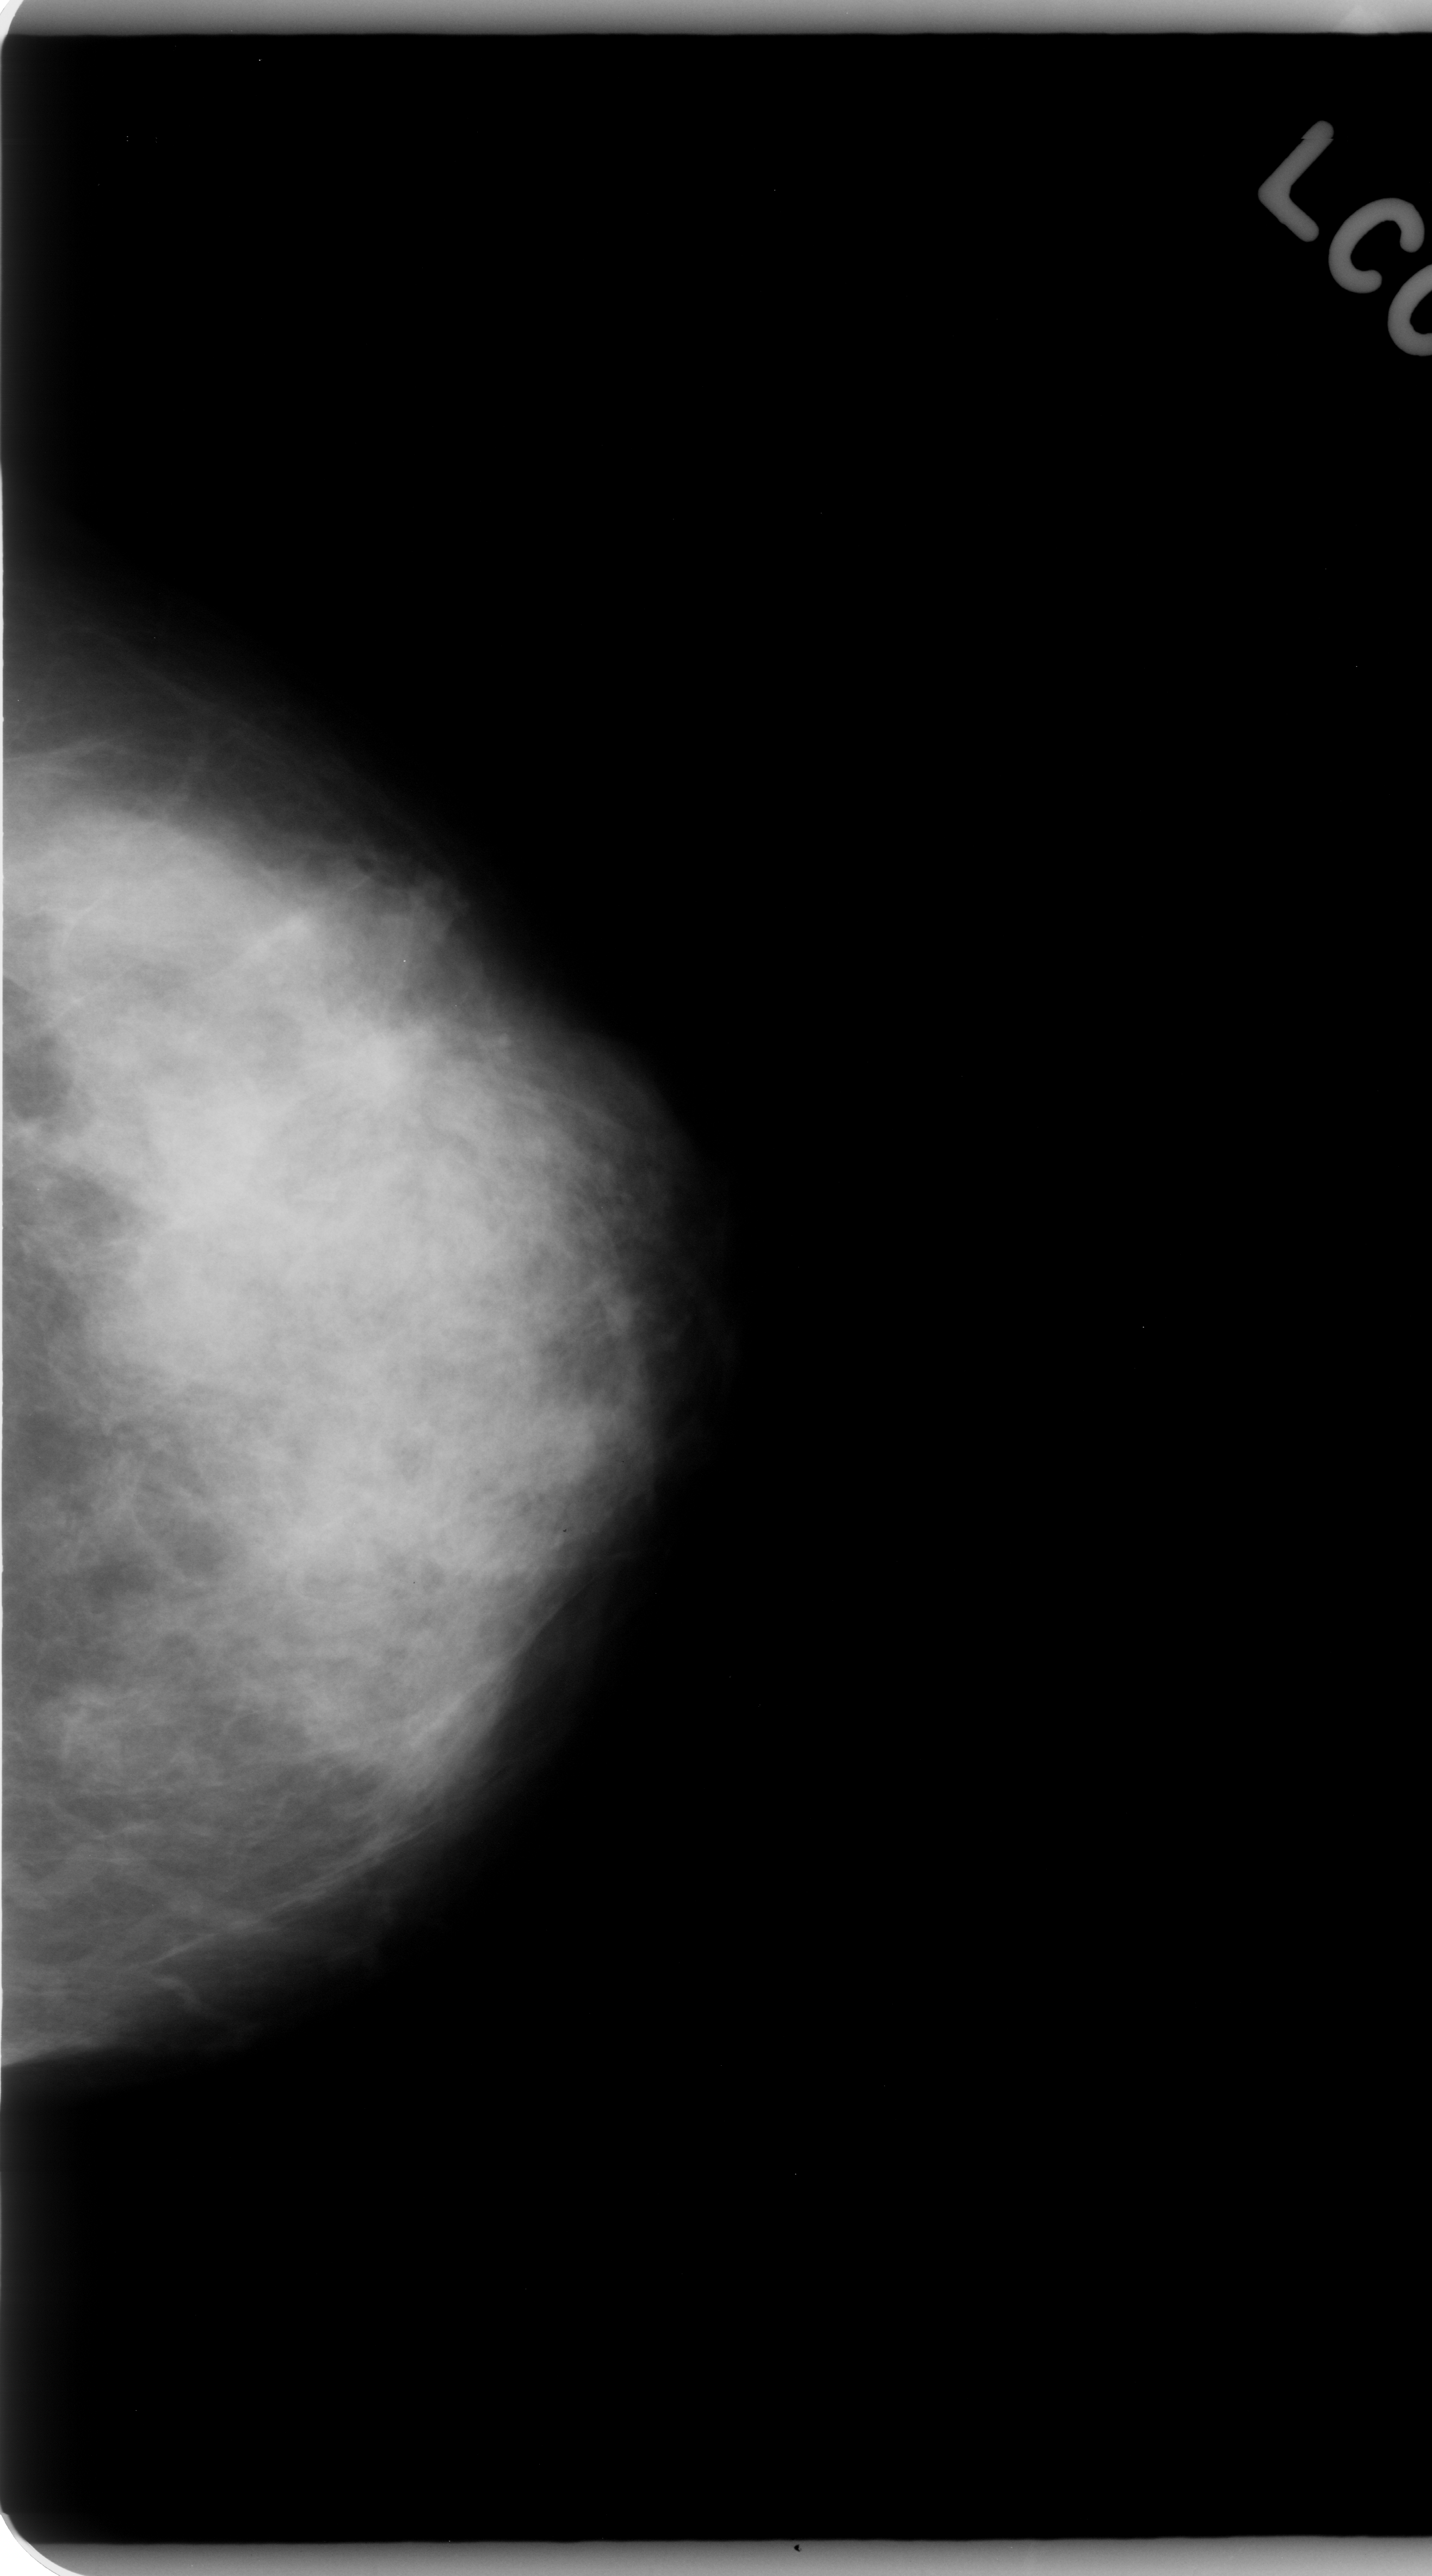
Scanned film-screen mammogram; left breast; CC view; 1432 × 2576 image matrix.
Expert-marked regions of interest on this image (one box per marked abnormality):
- mass, shape irregular, margins spiculated; BI-RADS assessment category 5; subtlety rating 4 on a 1 (subtle) to 5 (obvious) scale; pathology result (as recorded, not read from the image): malignant: bounding box (x1, y1, x2, y2) in pixels: (290, 973, 464, 1149)